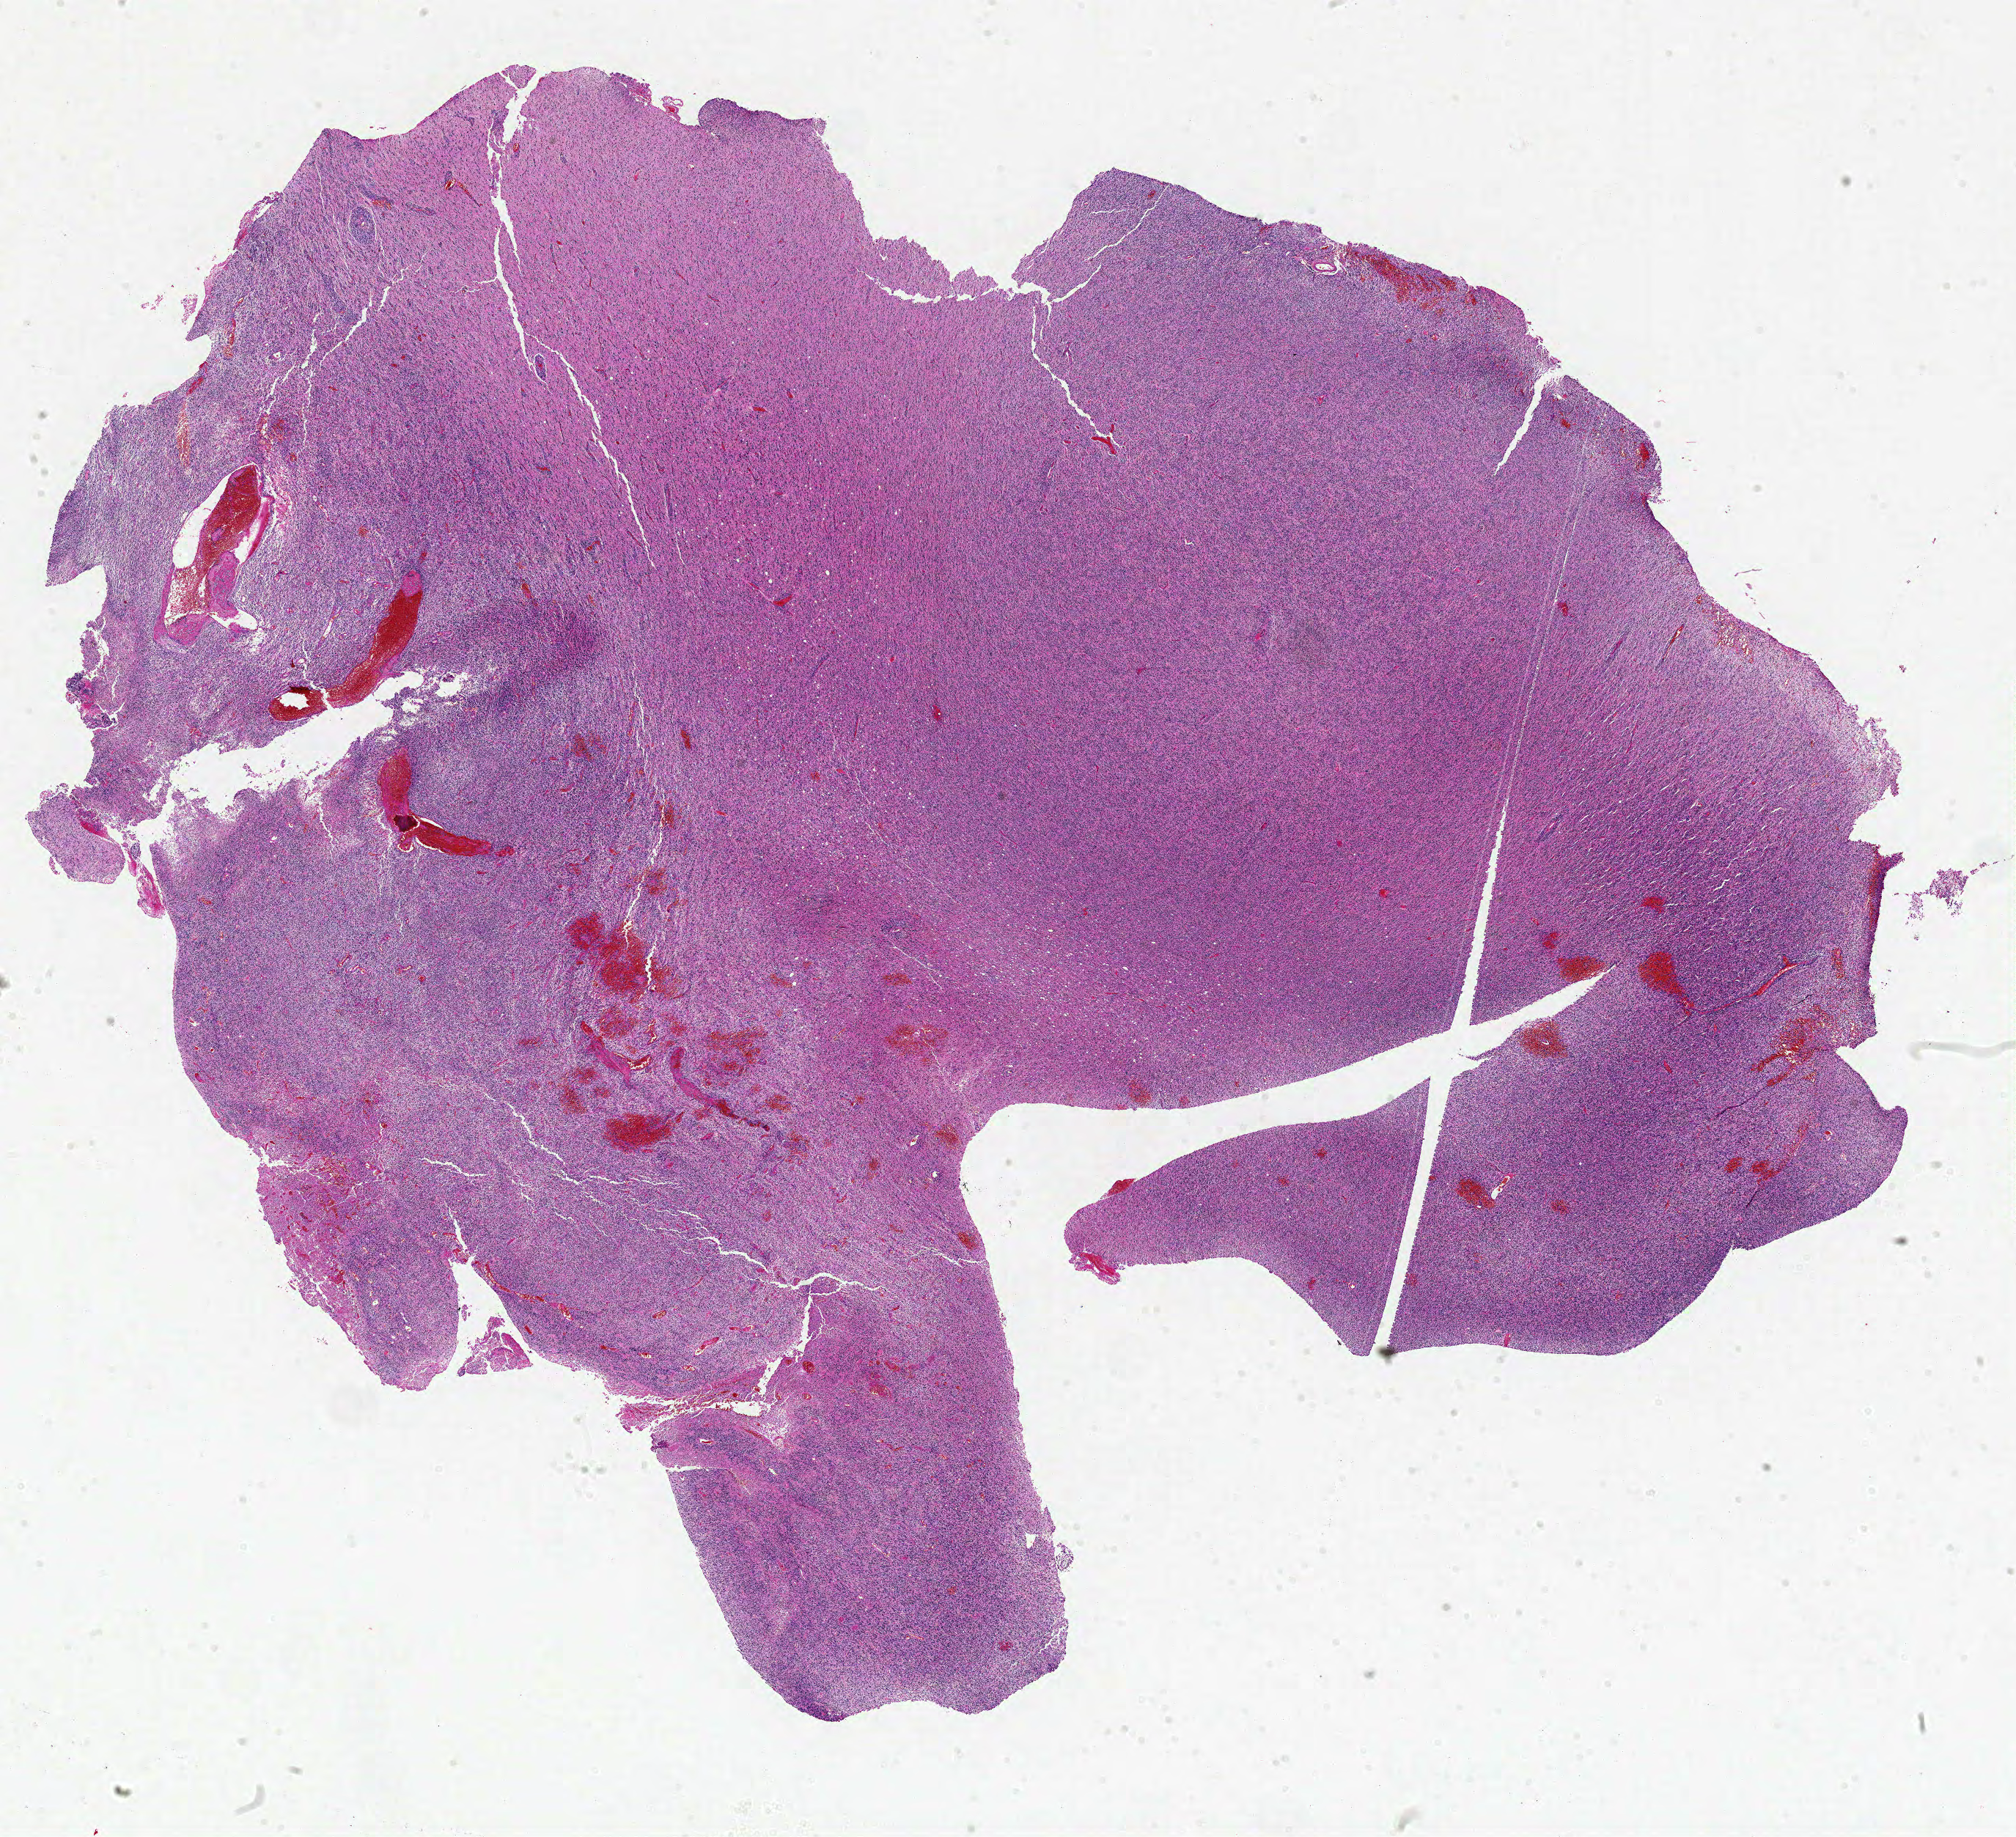
Digitized H&E-stained tissue section (whole slide), shown as a low-resolution overview of the whole scanned area (about 22.0 x 20.0 mm, acquisition: 20x scan), formalin-fixed paraffin-embedded (FFPE) diagnostic section, sample: primary tumour, brain. Female patient; age at initial diagnosis 61 years.
Histologic diagnosis: Glioblastoma.